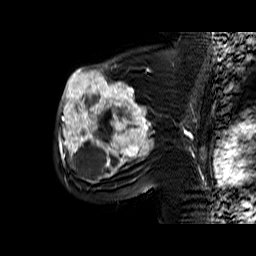
Breast MRI (dynamic contrast-enhanced), one sagittal slice. Position 39 of 60 along the scan axis. Dynamic contrast-enhanced series, time point 2 of 6 at this slice position (early post-contrast). 1.5 T. TE 6.4 ms, TR 32.9 ms. 4 mm slice thickness. 256 × 256 image matrix. Female patient. Case-level facts recorded for this patient, not image findings: setting: breast cancer imaged before/during neoadjuvant chemotherapy; receptor status: triple-negative.
Annotated regions visible in this slice (semi-automatic segmentation, software-assisted and operator-edited):
- analysis volume of interest (the breast-tissue region the enhancement analysis was run in; not a lesion): bounding box <56,65,159,174> (left, top, right, bottom; pixels)
- tumour enhancement mask (voxels above the 100 % enhancement threshold inside the analysis volume of interest): <59,65,154,174>